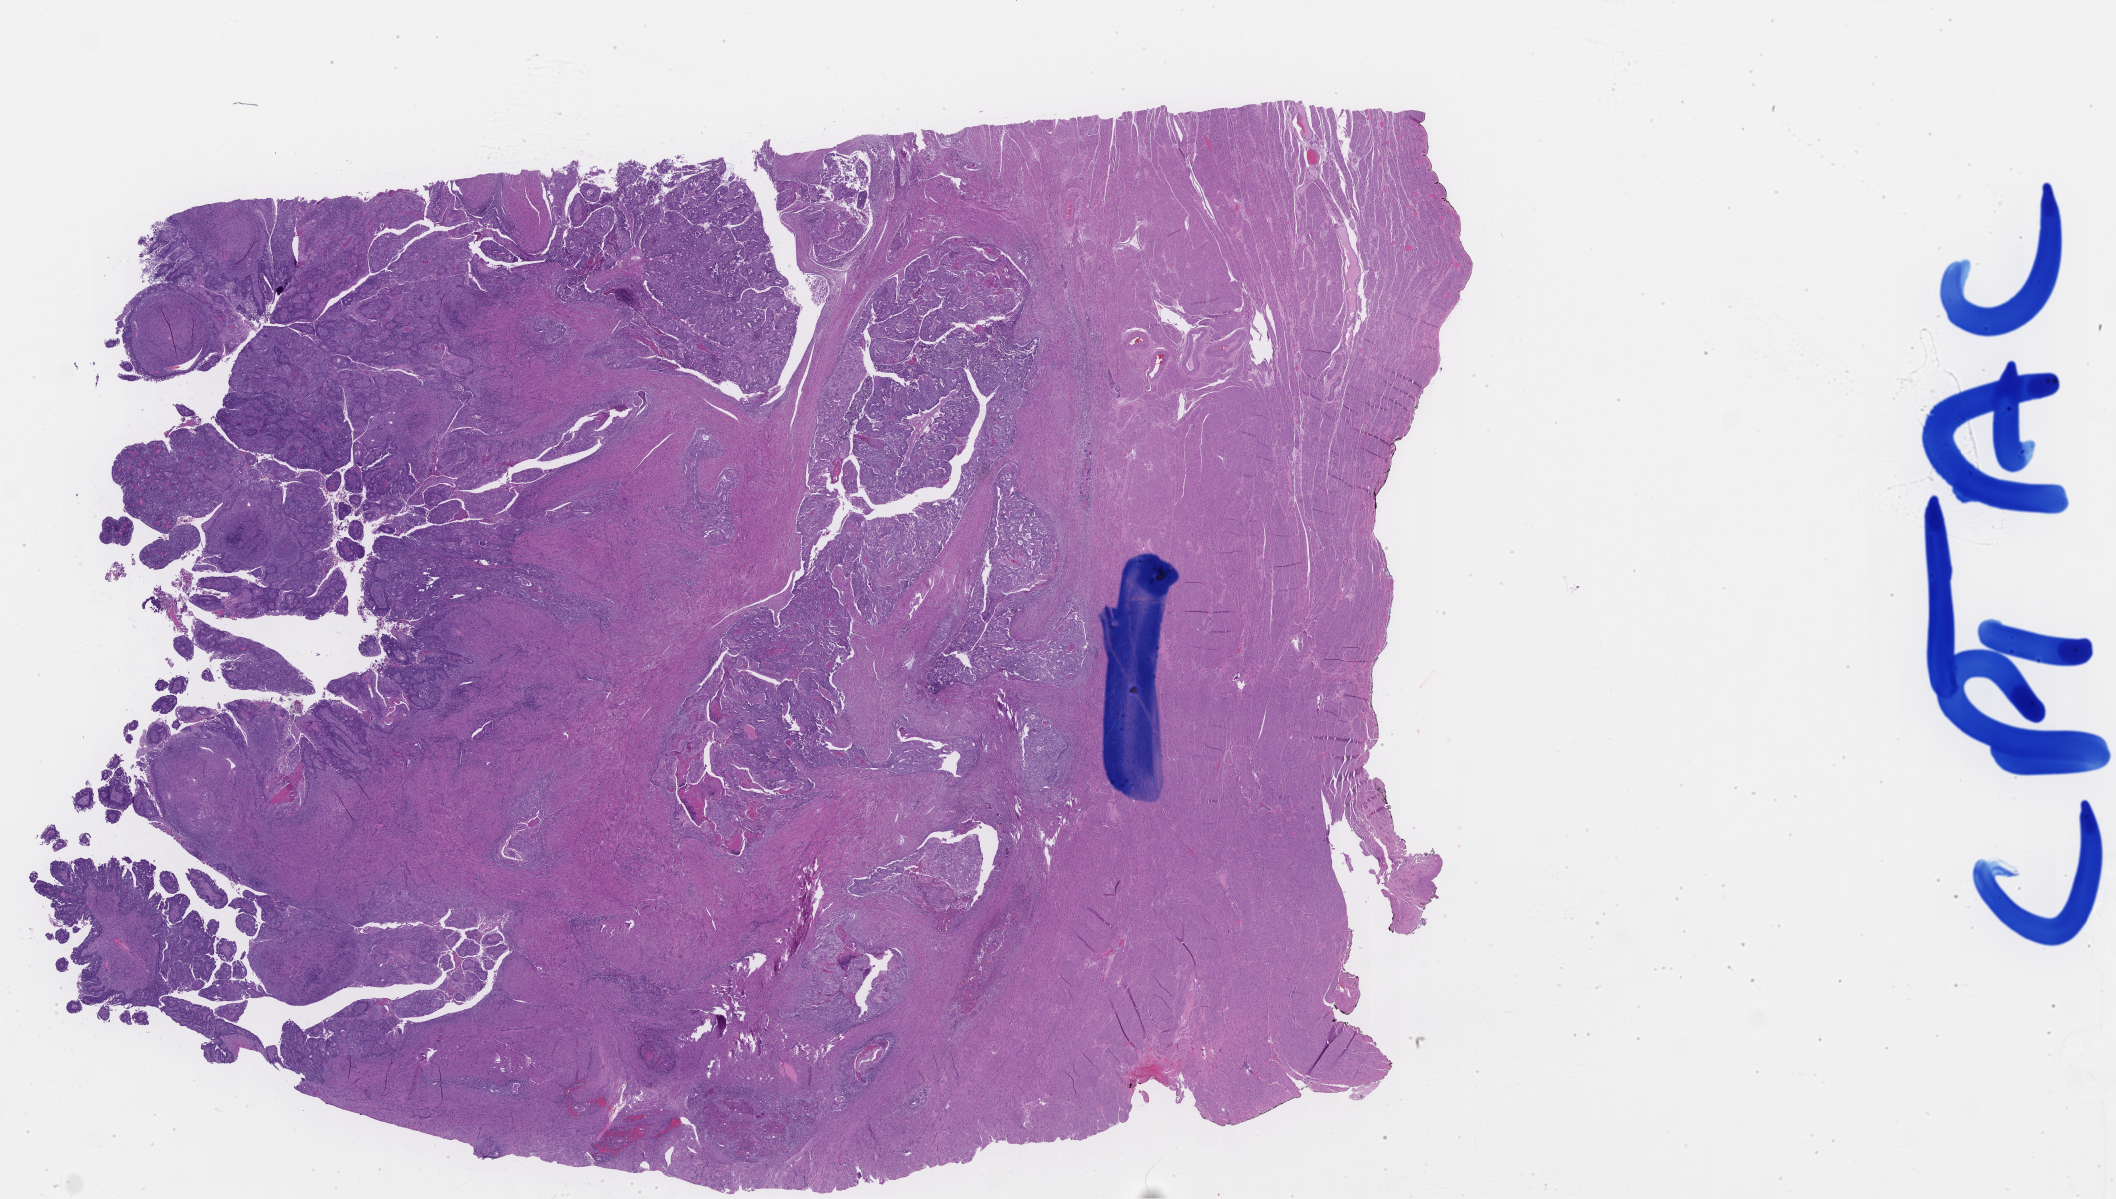
Whole-slide histology image, H&E, low-resolution overview of the scanned area, about 34.1 x 19.3 mm, uterus, tumour tissue. Patient: female, age 68 years.
Patient diagnosis (cohort enrolment): corpus endometrial carcinoma (uterus).